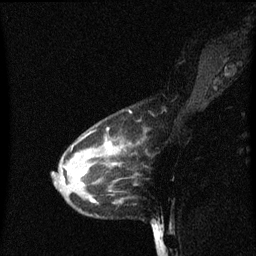
Breast MRI (dynamic contrast-enhanced), one sagittal slice; position 45 of 60 along the scan axis; dynamic contrast-enhanced series, image 2 of 3 at this slice position (ordered by acquisition); 1.5 T; TE 4.2 ms, TR 8.4 ms; 2 mm slice thickness; 256 × 256 image matrix, field of view 200 × 200 mm. Patient: female, 38 years. Case-level facts recorded for this patient, not image findings: setting: breast cancer imaged before/during neoadjuvant chemotherapy; receptor status: HR-positive, HER2-negative.
Structures marked on this image (semi-automatically segmented with operator editing):
- analysis volume of interest (the breast-tissue region the enhancement analysis was run in; not a lesion): bounding box <52,122,137,205> (left, top, right, bottom; pixels)
- tumour enhancement mask (voxels above the 70 % enhancement threshold inside the analysis volume of interest): <68,144,113,171>